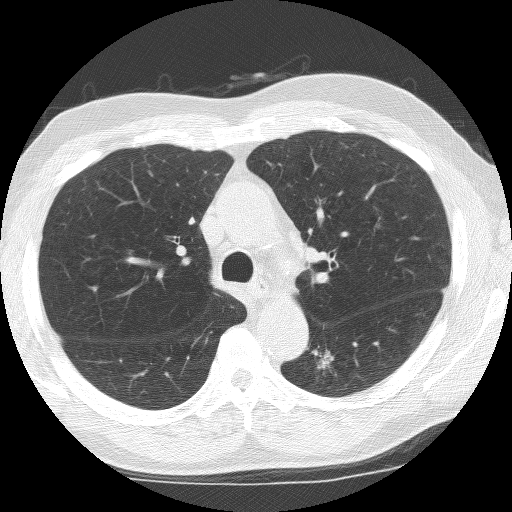
Axial slice from a low-dose chest CT screening exam; baseline screening round; lung window (W 1500 / L -600 HU); 2.5 mm slice thickness; lung (sharp) reconstruction kernel (BONE); 512 × 512 image matrix, field of view 323 × 323 mm. Male, age 67 years at enrolment. Current smoker at enrolment.
- Expert-annotated lung lesion, box from (x=293, y=341) to (x=342, y=388) px.
- Screening reader's record for this exam (one nodule recorded; not confirmed to be the boxed lesion): non-calcified nodule or mass ≥4 mm, left lower lobe, 18 × 13 mm, spiculated (stellate) margins, soft tissue attenuation.
- Official screen result: positive, change unspecified: nodule(s) >= 4 mm or enlarging nodule(s), mass(es), or other non-specific abnormalities suspicious for lung cancer.
- Lung cancer was diagnosed 5 days after this screen: non-small cell carcinoma, left lower lobe, undifferentiated (G4), stage IA (AJCC 6th edition), 12 mm at pathology.